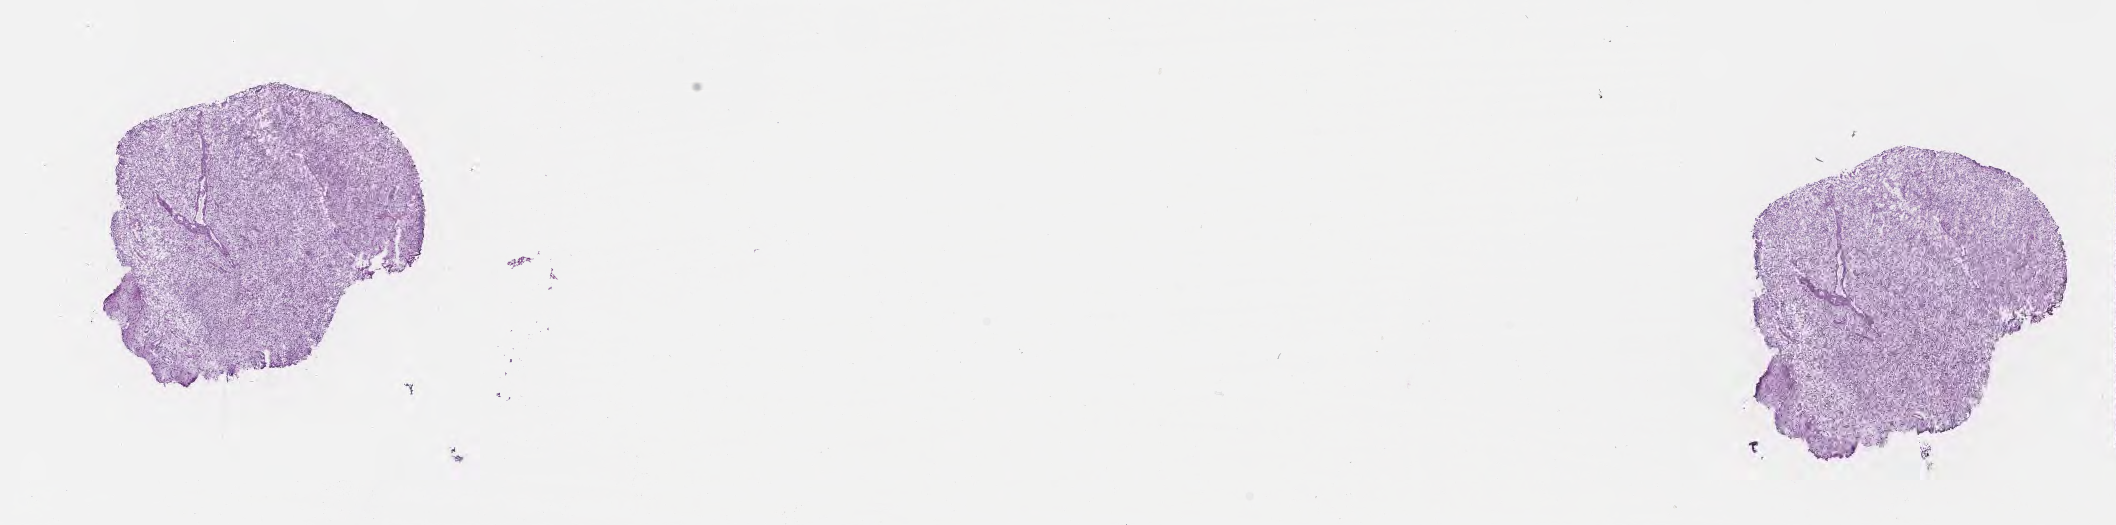
Haematoxylin and eosin whole-slide image — low-resolution overview of the scanned area, about 17.1 x 4.2 mm, frozen section, specimen: primary tumor, site: brain. Male, age 59 years at initial diagnosis. Pathologist review of this section (percent, as recorded): tumor cells 83%, tumor nuclei 86%, stromal cells 4%, necrosis 0%, normal cells 13%. Infiltration values recorded for this section: lymphocyte infiltration 0%, monocyte infiltration 0%, neutrophil infiltration 0%.
Histologic diagnosis: Glioblastoma, NOS. Section: bottom of the tissue portion.